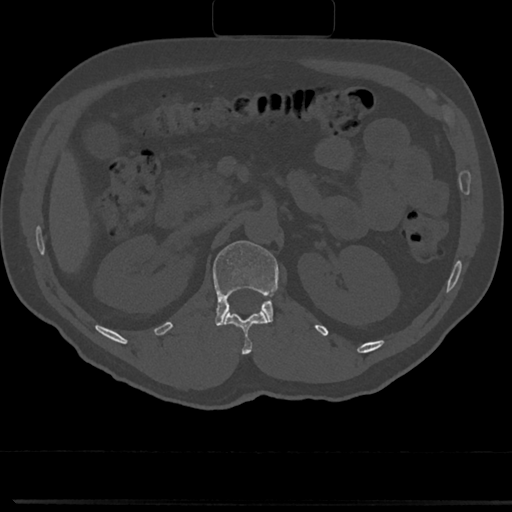
CT including the spine, one axial slice. Slice 105 of 817 in the series (ordered by position). Reconstruction kernel Br40s/3. 120 kVp. Bone window (W 1800 / L 400 HU). 0.5 mm slice thickness. 512 × 512 image matrix. Male patient, age 61 years. From the clinical record (not read from this slice): primary cancer: prostate.
Outlined on this slice (semi-automatically segmented with operator editing):
- L1 vertebra: box from (x=192, y=240) to (x=278, y=326) px
- T12 vertebra: (x=224, y=311)–(x=268, y=353)